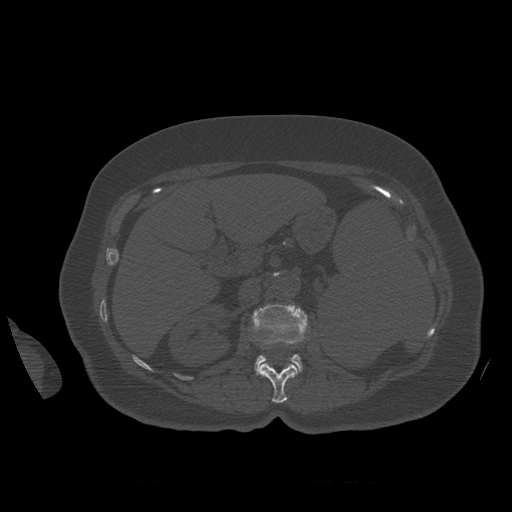
CT including the spine, one axial slice; slice 267 of 399 in the series (ordered by position); 120 kVp; bone window (W 1800 / L 400 HU); 1.25 mm slice thickness; 512 × 512 image matrix. Patient age 81 years. From the clinical record (not read from this slice): primary cancer: renal; vertebrae with lytic lesions (as recorded): L1.
Structures marked on this image (semi-automatically segmented with operator editing):
- L1 vertebra: bounding box (x1, y1, x2, y2) in pixels: (261, 363, 298, 403)
- L2 vertebra: (252, 304, 310, 376)